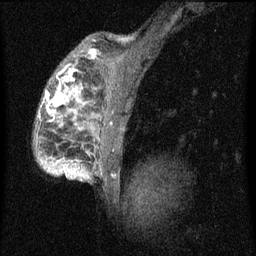
Breast MRI (dynamic contrast-enhanced), one sagittal slice; position 49 of 60 along the scan axis; dynamic contrast-enhanced series, image 2 of 4 at this slice position (ordered by acquisition); 1.5 T; TE 4.2 ms, TR 8 ms; 2 mm slice thickness; 256 × 256 image matrix, field of view 180 × 180 mm. Female patient, age 50 years.
Outlined on this slice (semi-automatically segmented with operator editing):
- analysis volume of interest (the breast-tissue region the enhancement analysis was run in; not a lesion): bounding box (x1, y1, x2, y2) in pixels: (34, 44, 124, 177)
- tumour enhancement mask (voxels above the 70 % enhancement threshold inside the analysis volume of interest): (46, 54, 95, 165)